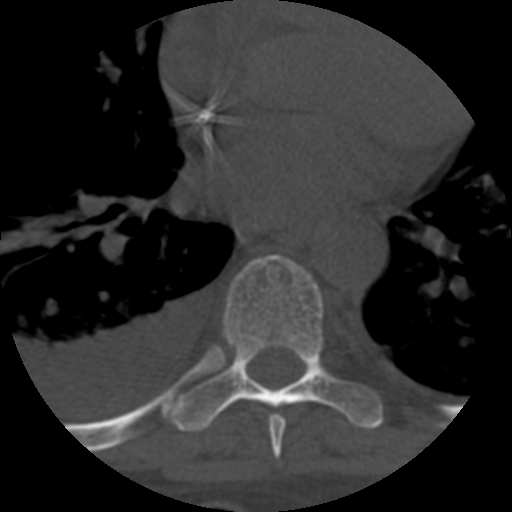
CT including the spine, one axial slice; position 400 of 708 along the scan axis; reconstruction kernel STANDARD; 120 kVp; one of 3 acquisitions stored at this slice position; bone window (W 1800 / L 400 HU); 1.25 mm slice thickness; 512 × 512 image matrix, field of view 160 × 160 mm. Patient age 55 years. Case-level facts recorded for this patient, not image findings: primary cancer: colon.
Annotated regions visible in this slice (semi-automatically segmented with operator editing):
- T7 vertebra: box from (x=268, y=414) to (x=286, y=459) px
- T8 vertebra: (x=174, y=255)–(x=383, y=433)